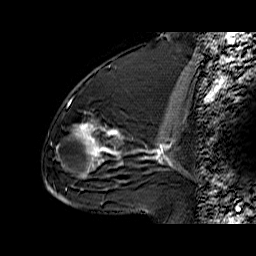
Breast MRI (dynamic contrast-enhanced), one sagittal slice. Slice 34 of 60 in the series (ordered by position). Dynamic contrast-enhanced series, time point 2 of 6 at this slice position (early post-contrast). 1.5 T. TE 6.3 ms, TR 32.9 ms. 256 × 256 image matrix, field of view 200 × 200 mm. Female patient. Case-level facts recorded for this patient, not image findings: setting: breast cancer imaged before/during neoadjuvant chemotherapy; receptor status: triple-negative.
Structures marked on this image (semi-automatically segmented with operator editing):
- analysis volume of interest (the breast-tissue region the enhancement analysis was run in; not a lesion): bounding box <55,76,130,170> (left, top, right, bottom; pixels)
- tumour enhancement mask (voxels above the 100 % enhancement threshold inside the analysis volume of interest): <74,123,121,166>